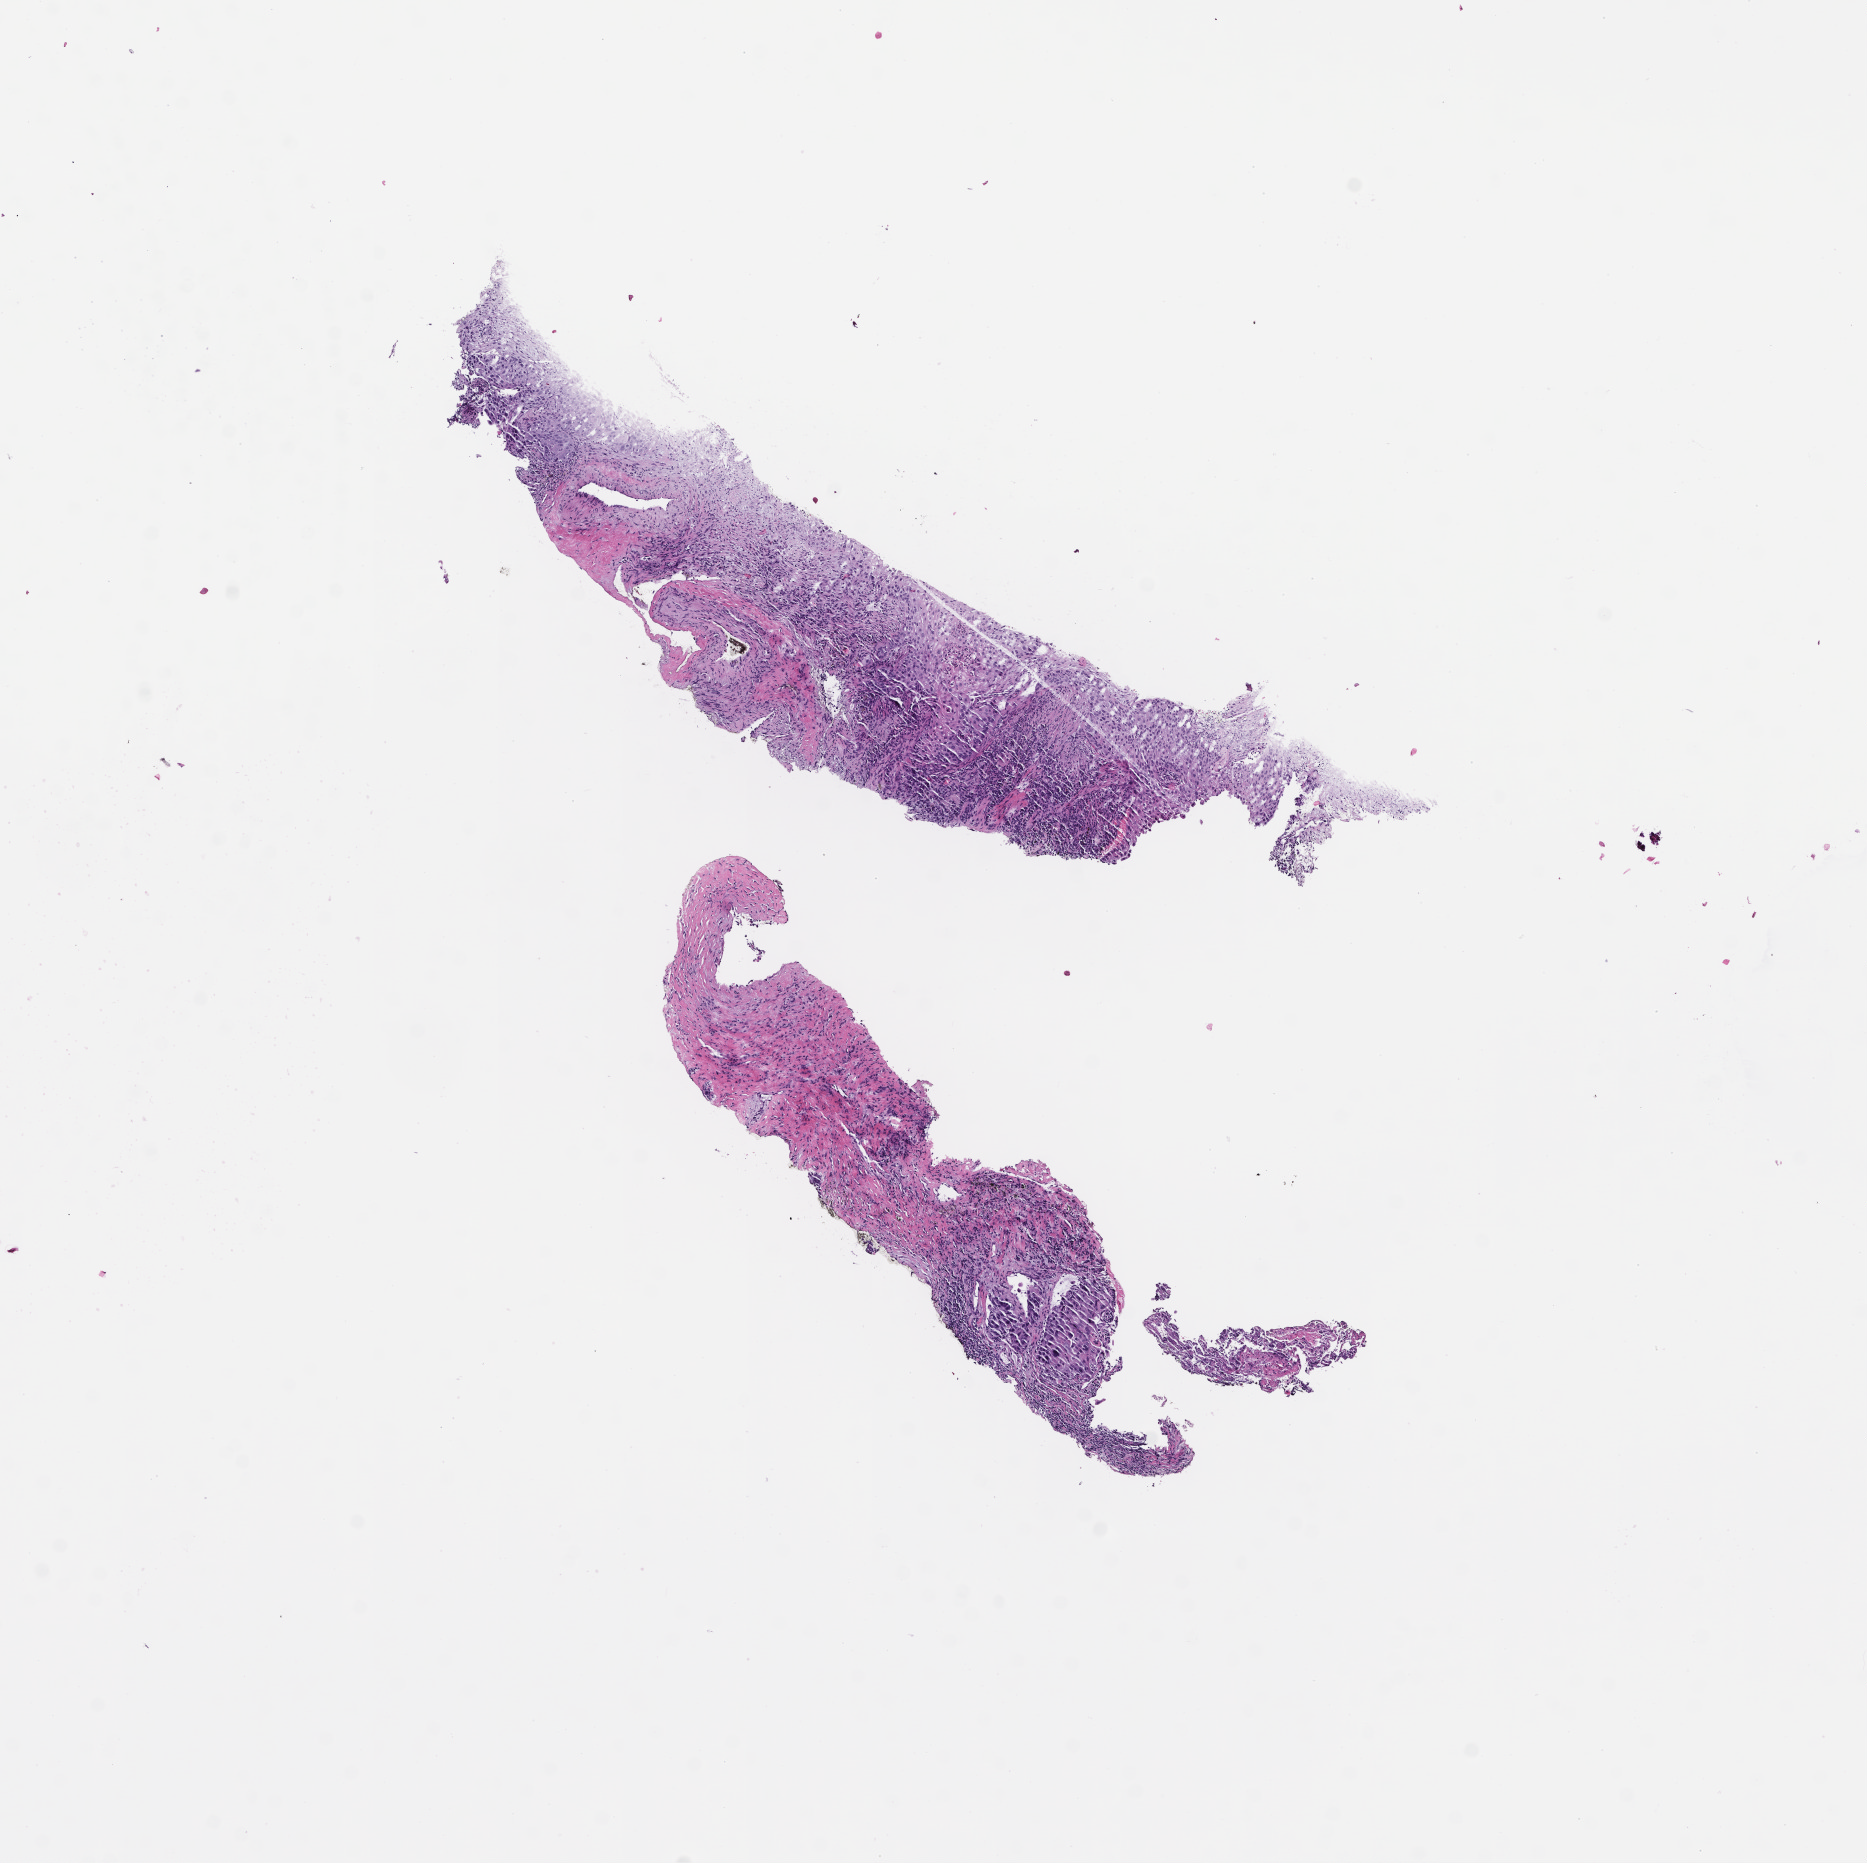
Whole-slide image, H&E stain, whole scanned area (about 7.5 x 7.5 mm) shown as a low-resolution overview. FFPE section. Site: lung. Archival tissue. Male patient.
• this section: primary tumor
• diagnosis: Non-Small Cell Lung Carcinoma